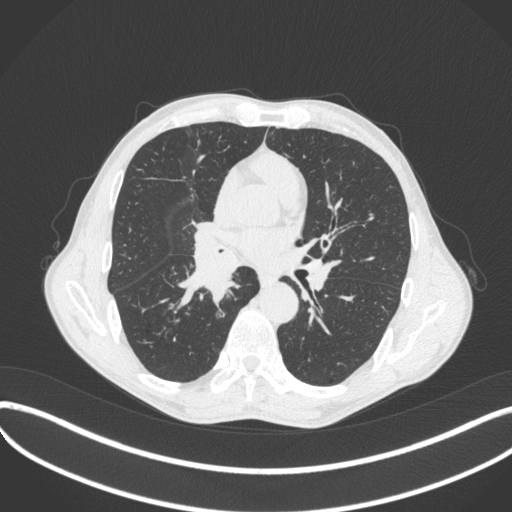
Chest CT, one axial slice; slice 228 of 481 in the series (ordered by position); lung window (W 1500 / L -600 HU); 512 × 512 image matrix. Patient: male, 65 years. Case-level facts recorded for this patient, not image findings: clinical TNM (as recorded): T2a N0 M0; histopathological grade: G2.
Outlined on this slice (bounding box drawn by a radiologist):
- lung tumour (recorded histology: squamous cell carcinoma): box from (x=169, y=230) to (x=245, y=318) px